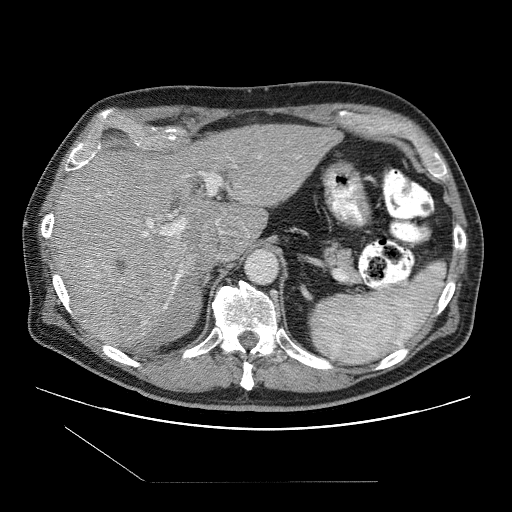
Contrast-enhanced abdominal CT (liver protocol), one axial slice; slice 68 of 109 in the series (ordered by position); reconstruction kernel STANDARD; 120 kVp; one of 2 acquisitions stored at this slice position; soft-tissue window (W 400 / L 40 HU); 512 × 512 image matrix, field of view 400 × 400 mm. From the clinical record (not read from this slice): diagnosis: hepatocellular carcinoma (patient treated with transarterial chemoembolisation; whether this scan precedes or follows treatment is not stated here); TNM stage (as recorded): Stage-IIIB; Child-Pugh class: A; tumour differentiation: well differentiated.
Structures marked on this image (semi-automatic segmentation, software-assisted and operator-edited):
- abdominal aorta: bounding box [x1, y1, x2, y2] px = [246, 250, 279, 284]
- liver parenchyma outside the tumour (the mass and vessels are separate outlines, so this box may not span the whole liver): [52, 124, 340, 346]
- mass: [60, 243, 180, 343]
- liver vessels: [97, 156, 260, 324]